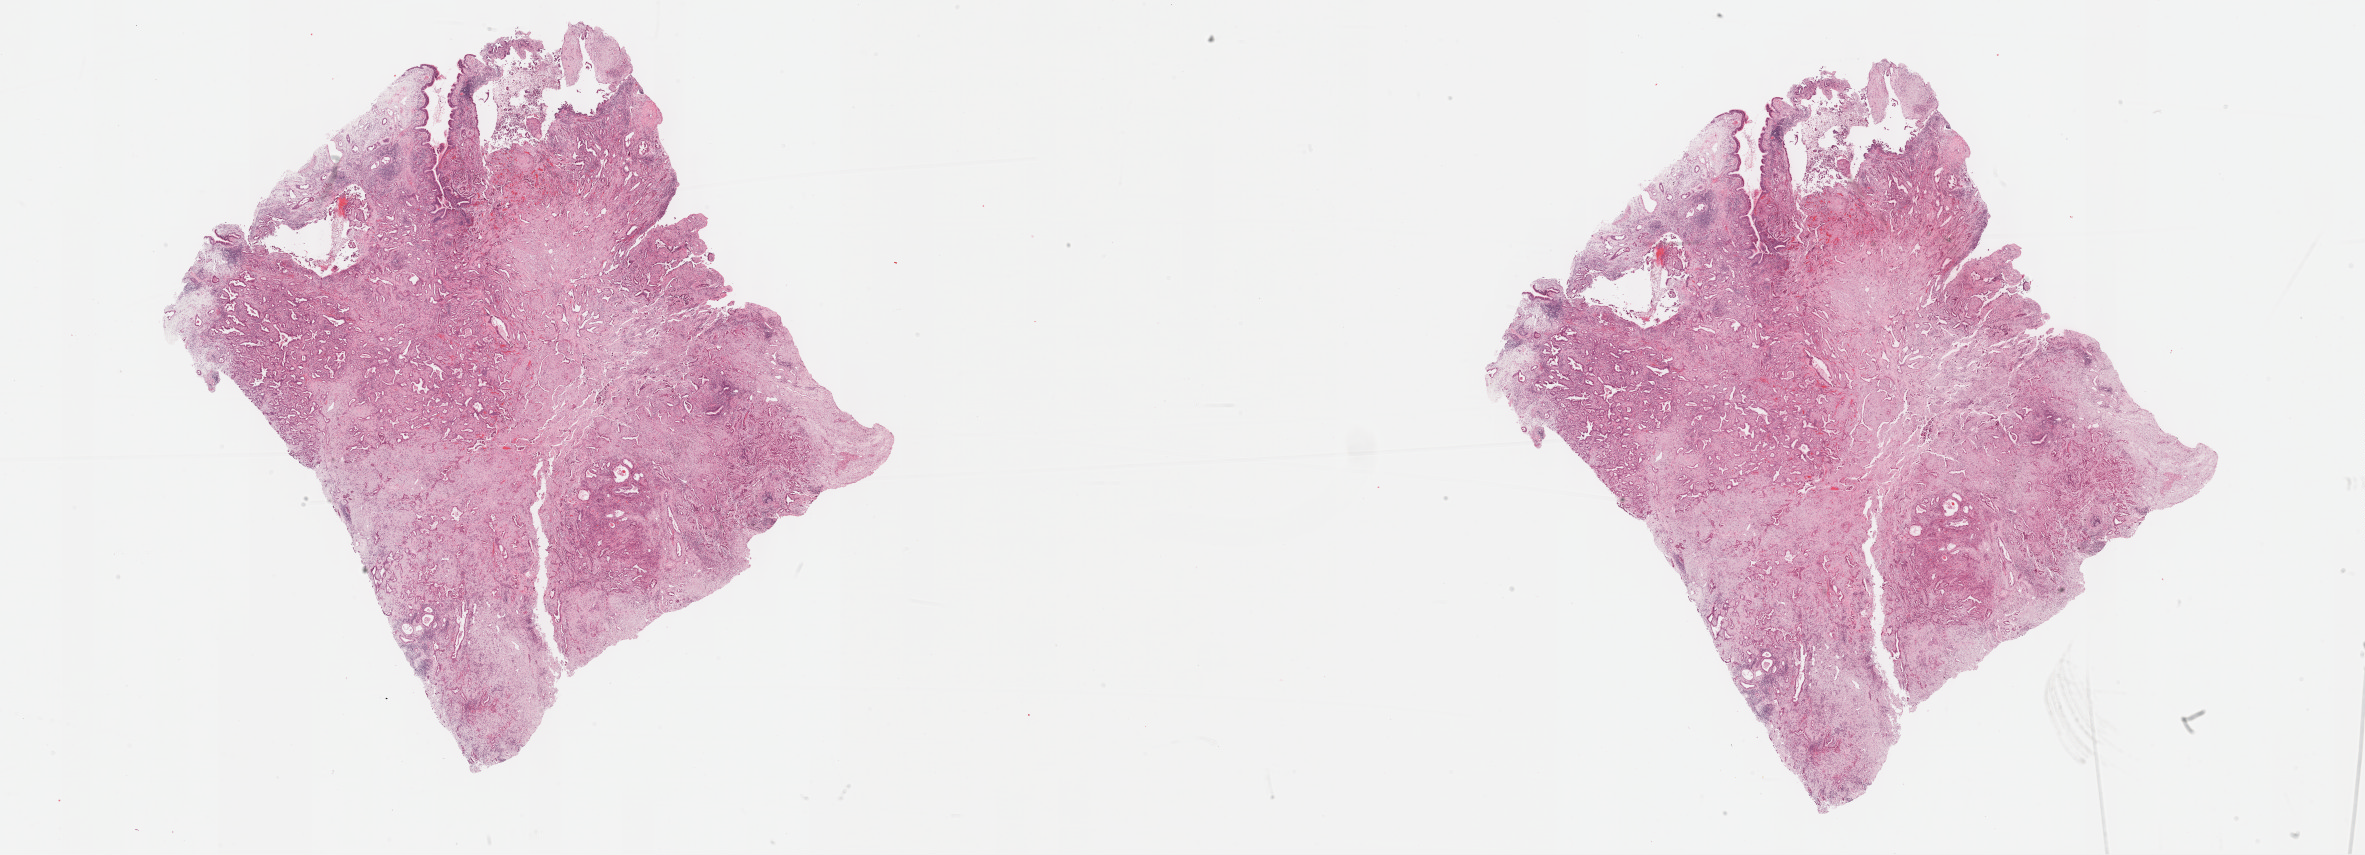
Digitized H&E-stained tissue section (whole slide), a low-resolution overview of the entire scanned area, about 38.3 x 13.8 mm. Formalin-fixed paraffin-embedded (FFPE) diagnostic section. Lung, primary tumour sample. Patient: female, age at initial diagnosis 82 years.
Histologic diagnosis: Adenocarcinoma, NOS (upper lobe, lung).